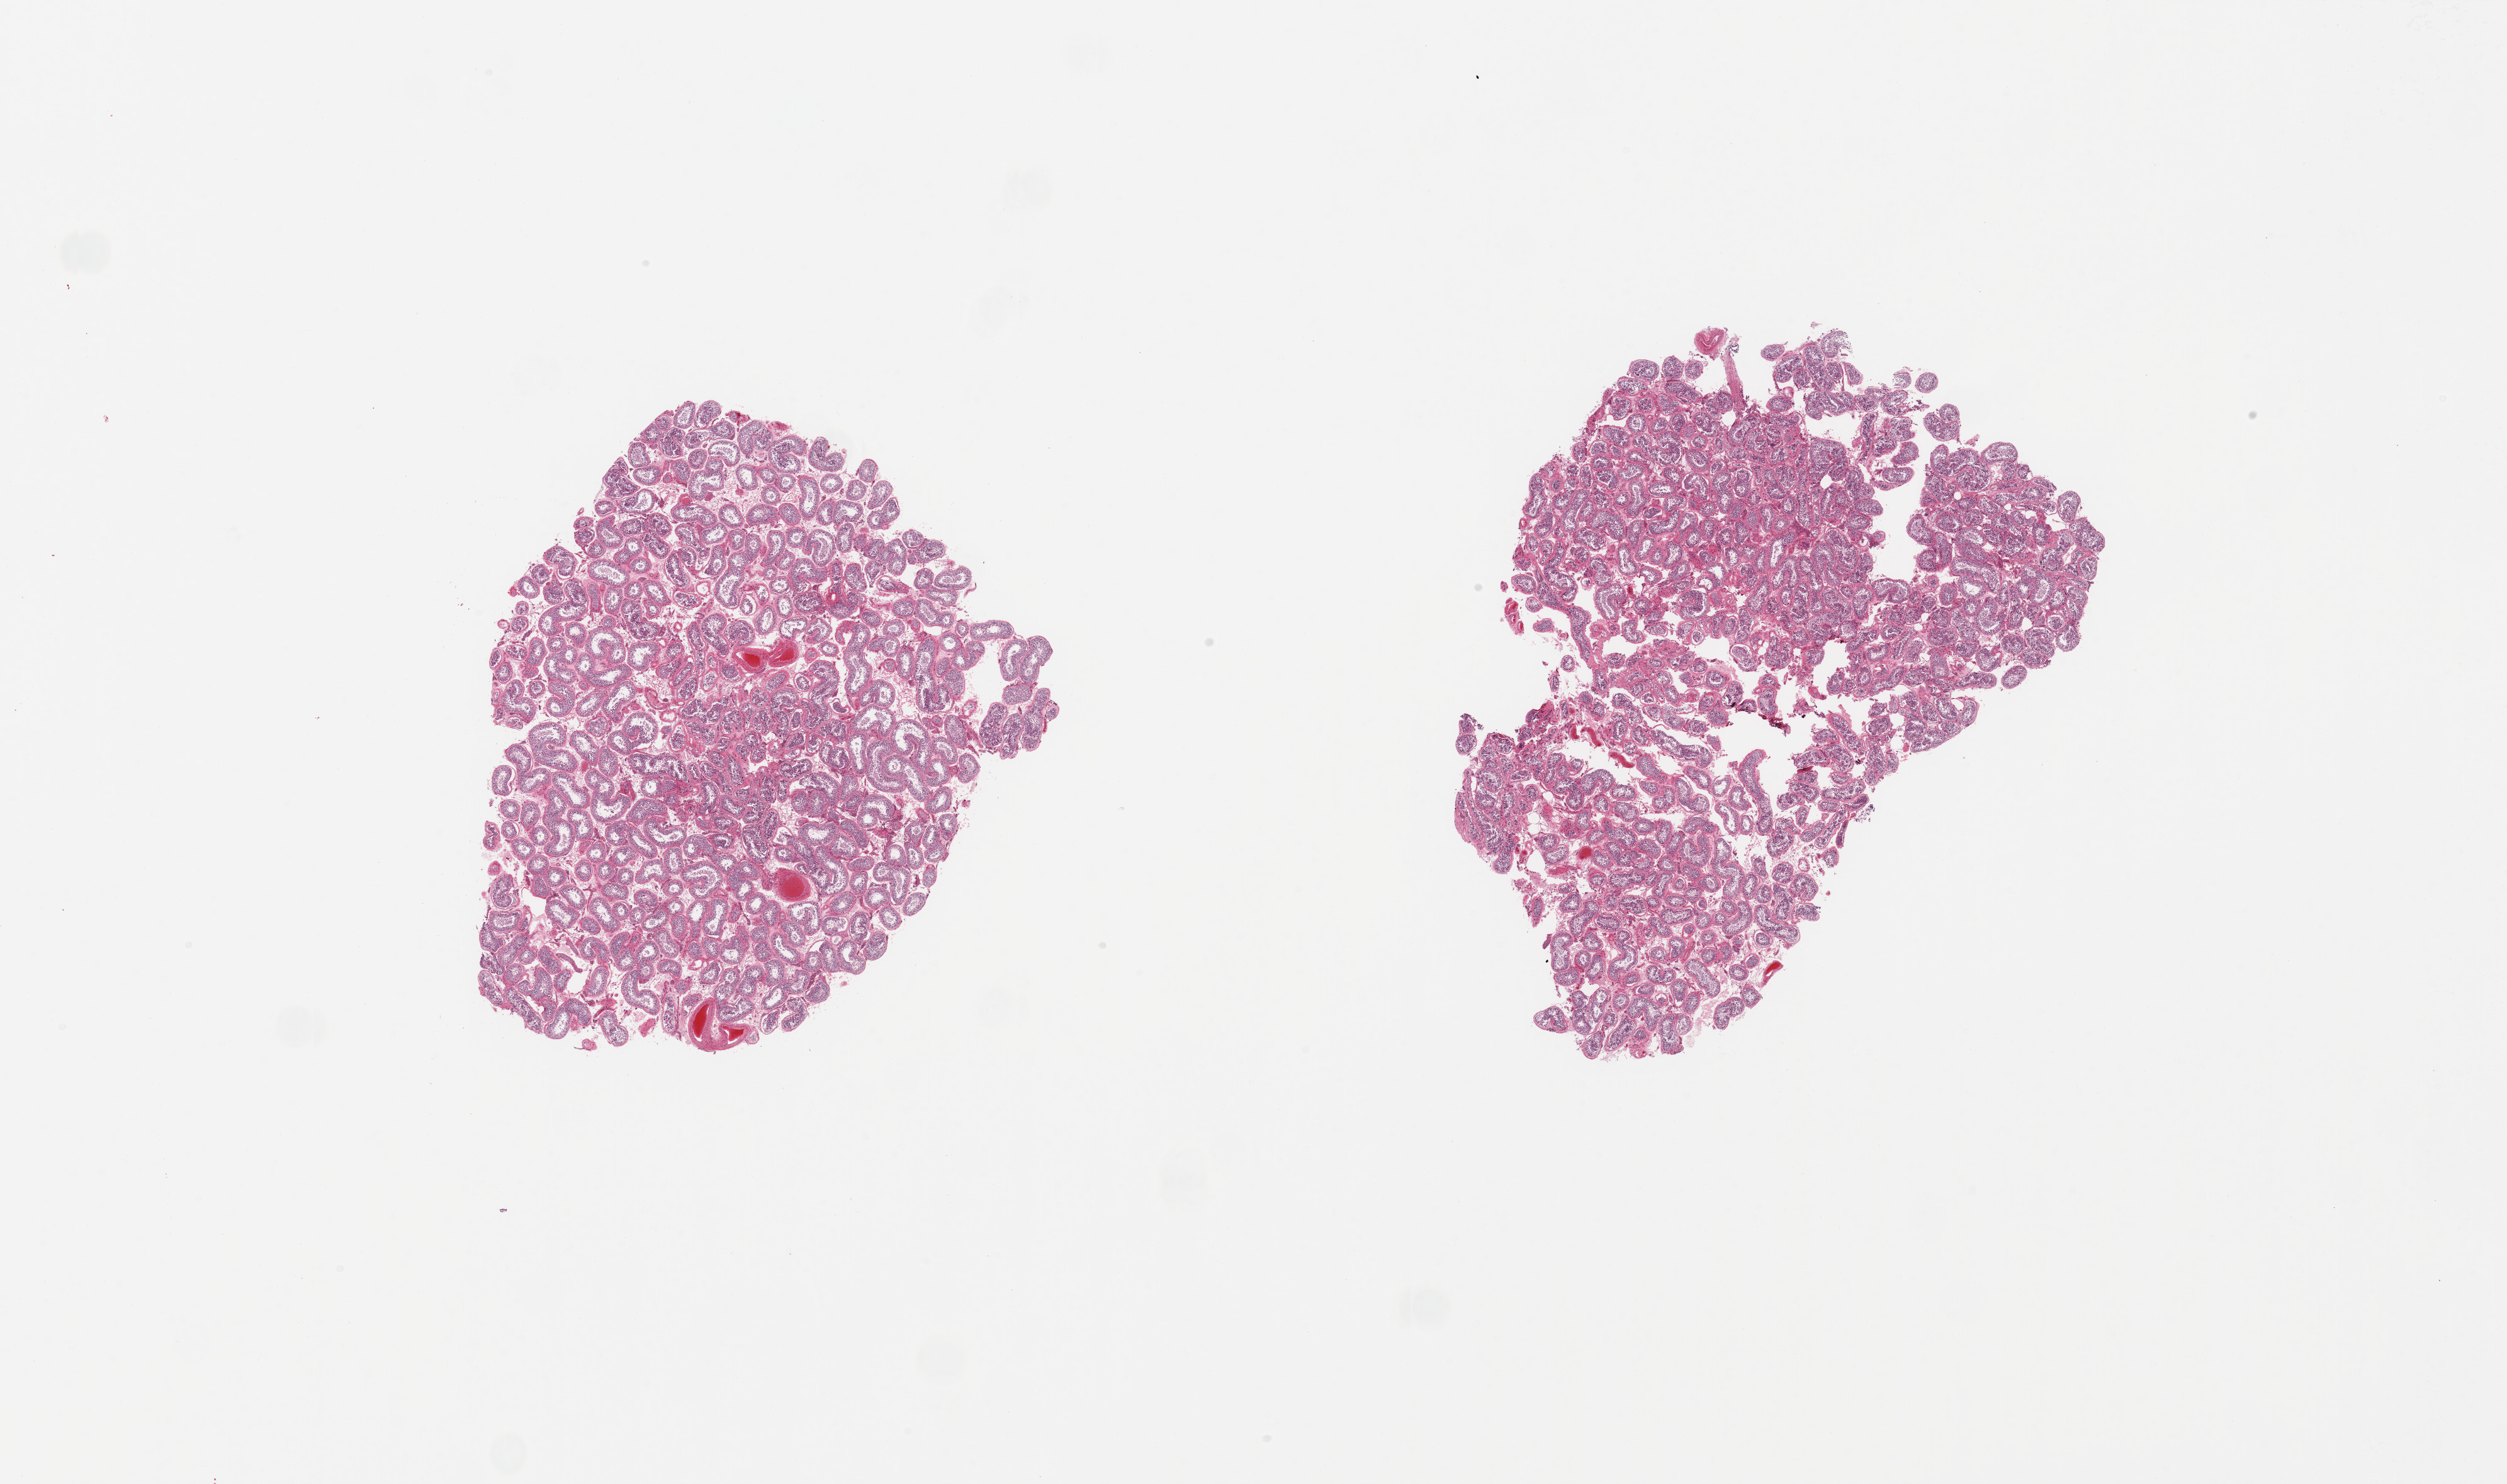
Whole-slide image, H&E stain, brightfield — low-resolution overview of the scanned area, about 31.5 x 18.6 mm. PAXgene-fixed paraffin-embedded (PFPE) section. Section of testis (target tissue). Donor tissue sample. Donor sex: male.
Pathologist's review note for this sample: 2 pieces, spermatogenesis appears reduced.